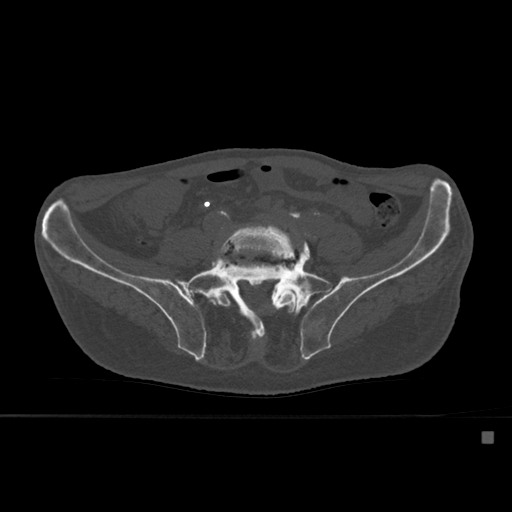
CT including the spine, one axial slice; slice 167 of 527 in the series (ordered by position); bone window (W 1800 / L 400 HU); 1.5 mm slice thickness; 512 × 512 image matrix. Patient: male, 78 years. Case-level facts recorded for this patient, not image findings: primary cancer: prostate.
Structures marked on this image (semi-automatically segmented with operator editing):
- L5 vertebra: bounding box <209,227,298,344> (left, top, right, bottom; pixels)